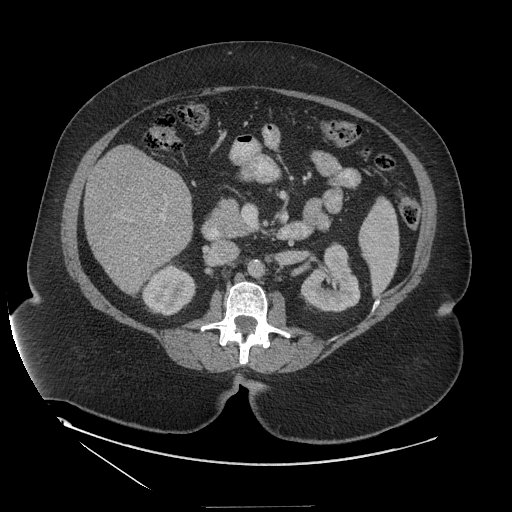
Contrast-enhanced abdominal CT (liver protocol), one axial slice; reconstruction kernel STANDARD; 140 kVp; soft-tissue window (W 400 / L 40 HU); 2.5 mm slice thickness; 512 × 512 image matrix, field of view 480 × 480 mm. From the clinical record (not read from this slice): diagnosis: hepatocellular carcinoma (patient treated with transarterial chemoembolisation; whether this scan precedes or follows treatment is not stated here); TNM stage (as recorded): Stage-II; Child-Pugh class: A; tumour differentiation: well differentiated; tumour nodularity: multinodular.
Annotated regions visible in this slice (semi-automatically segmented with operator editing):
- liver parenchyma outside the tumour (the mass and vessels are separate outlines, so this box may not span the whole liver): box from (x=84, y=145) to (x=192, y=293) px